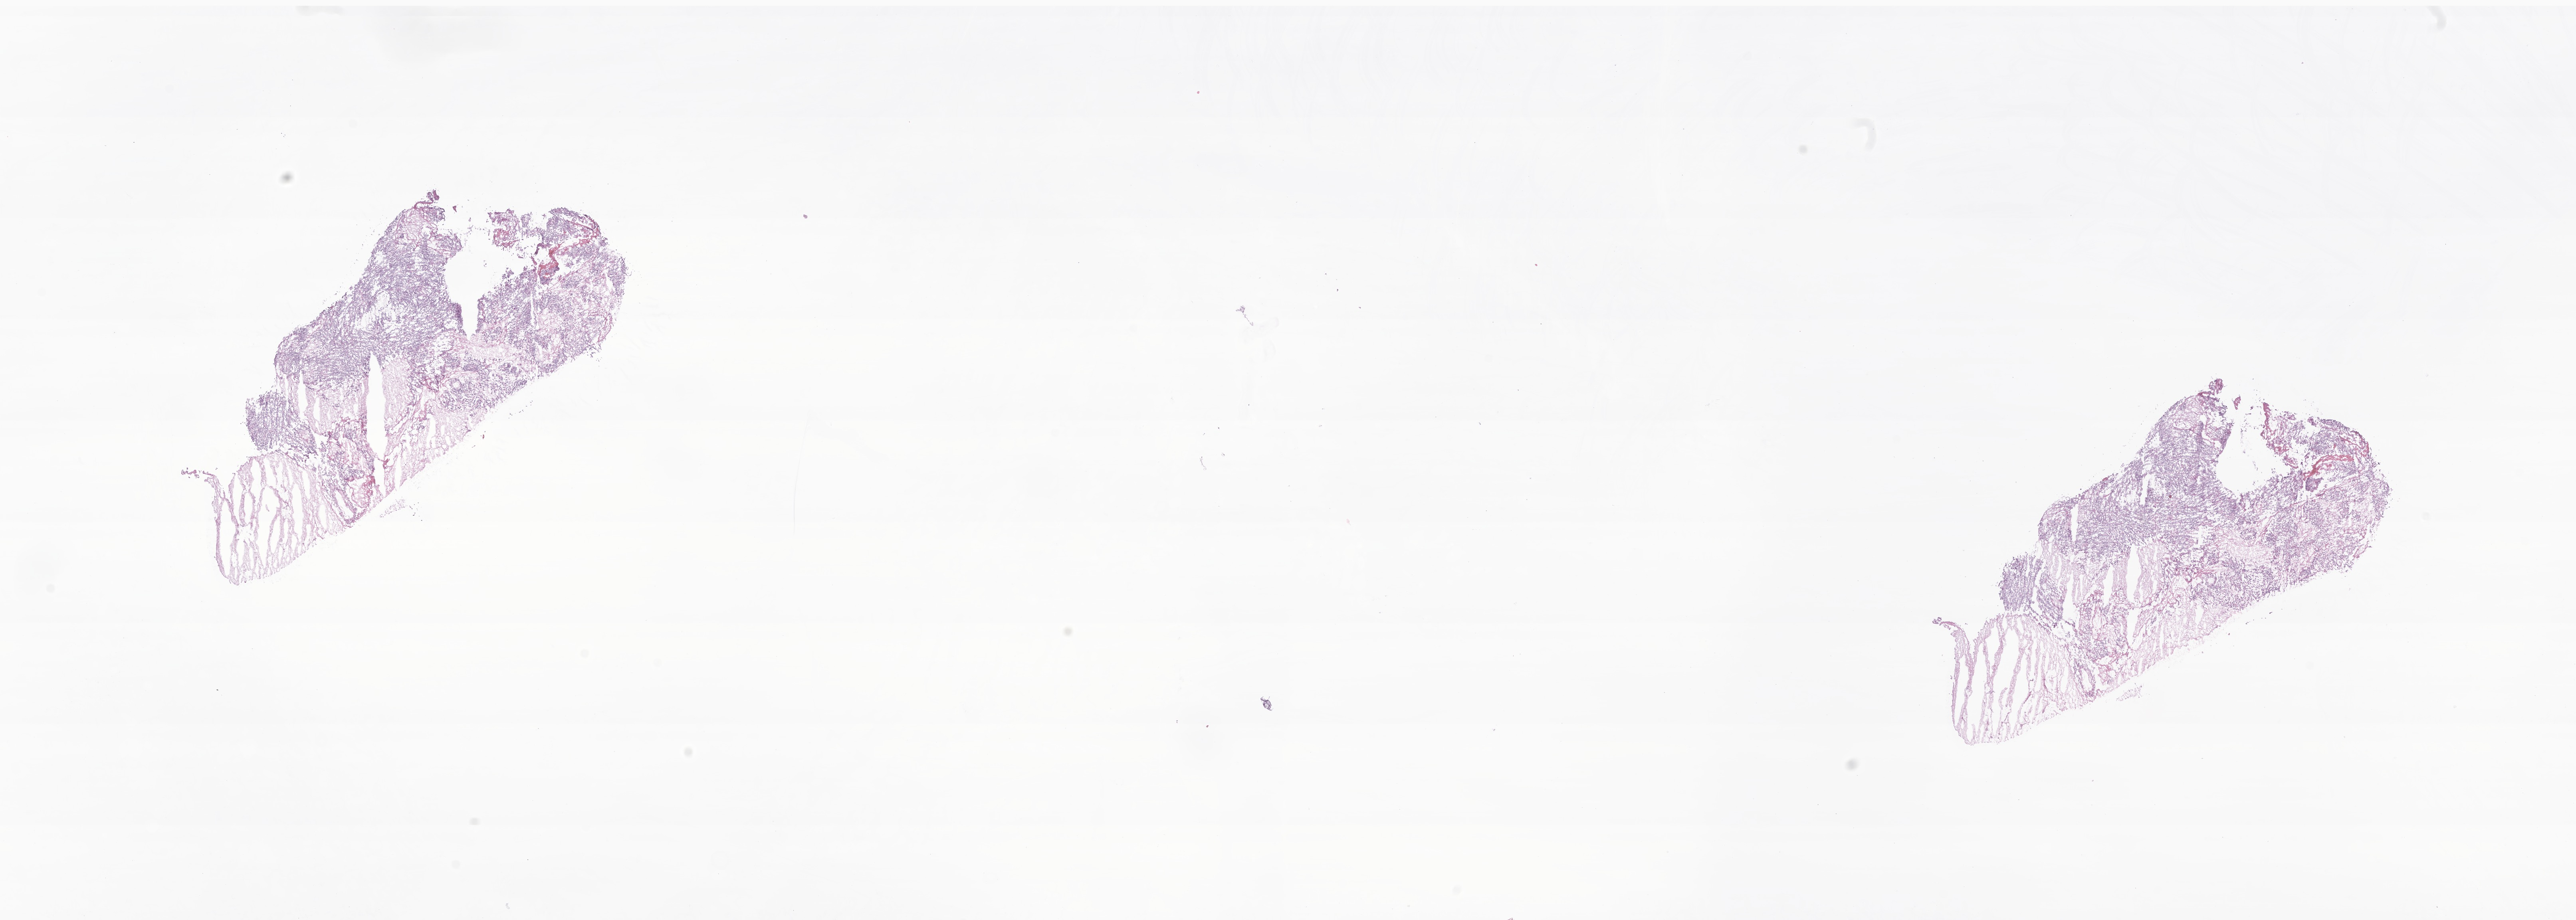
H&E whole-slide image of tumor tissue from the cerebellum, whole scanned area (about 27.2 x 9.7 mm) shown as a low-resolution overview, frozen section (OCT-embedded). Patient: female, age 106 months (8 years 10 months).
Recorded diagnosis: Medulloblastoma, NOS.